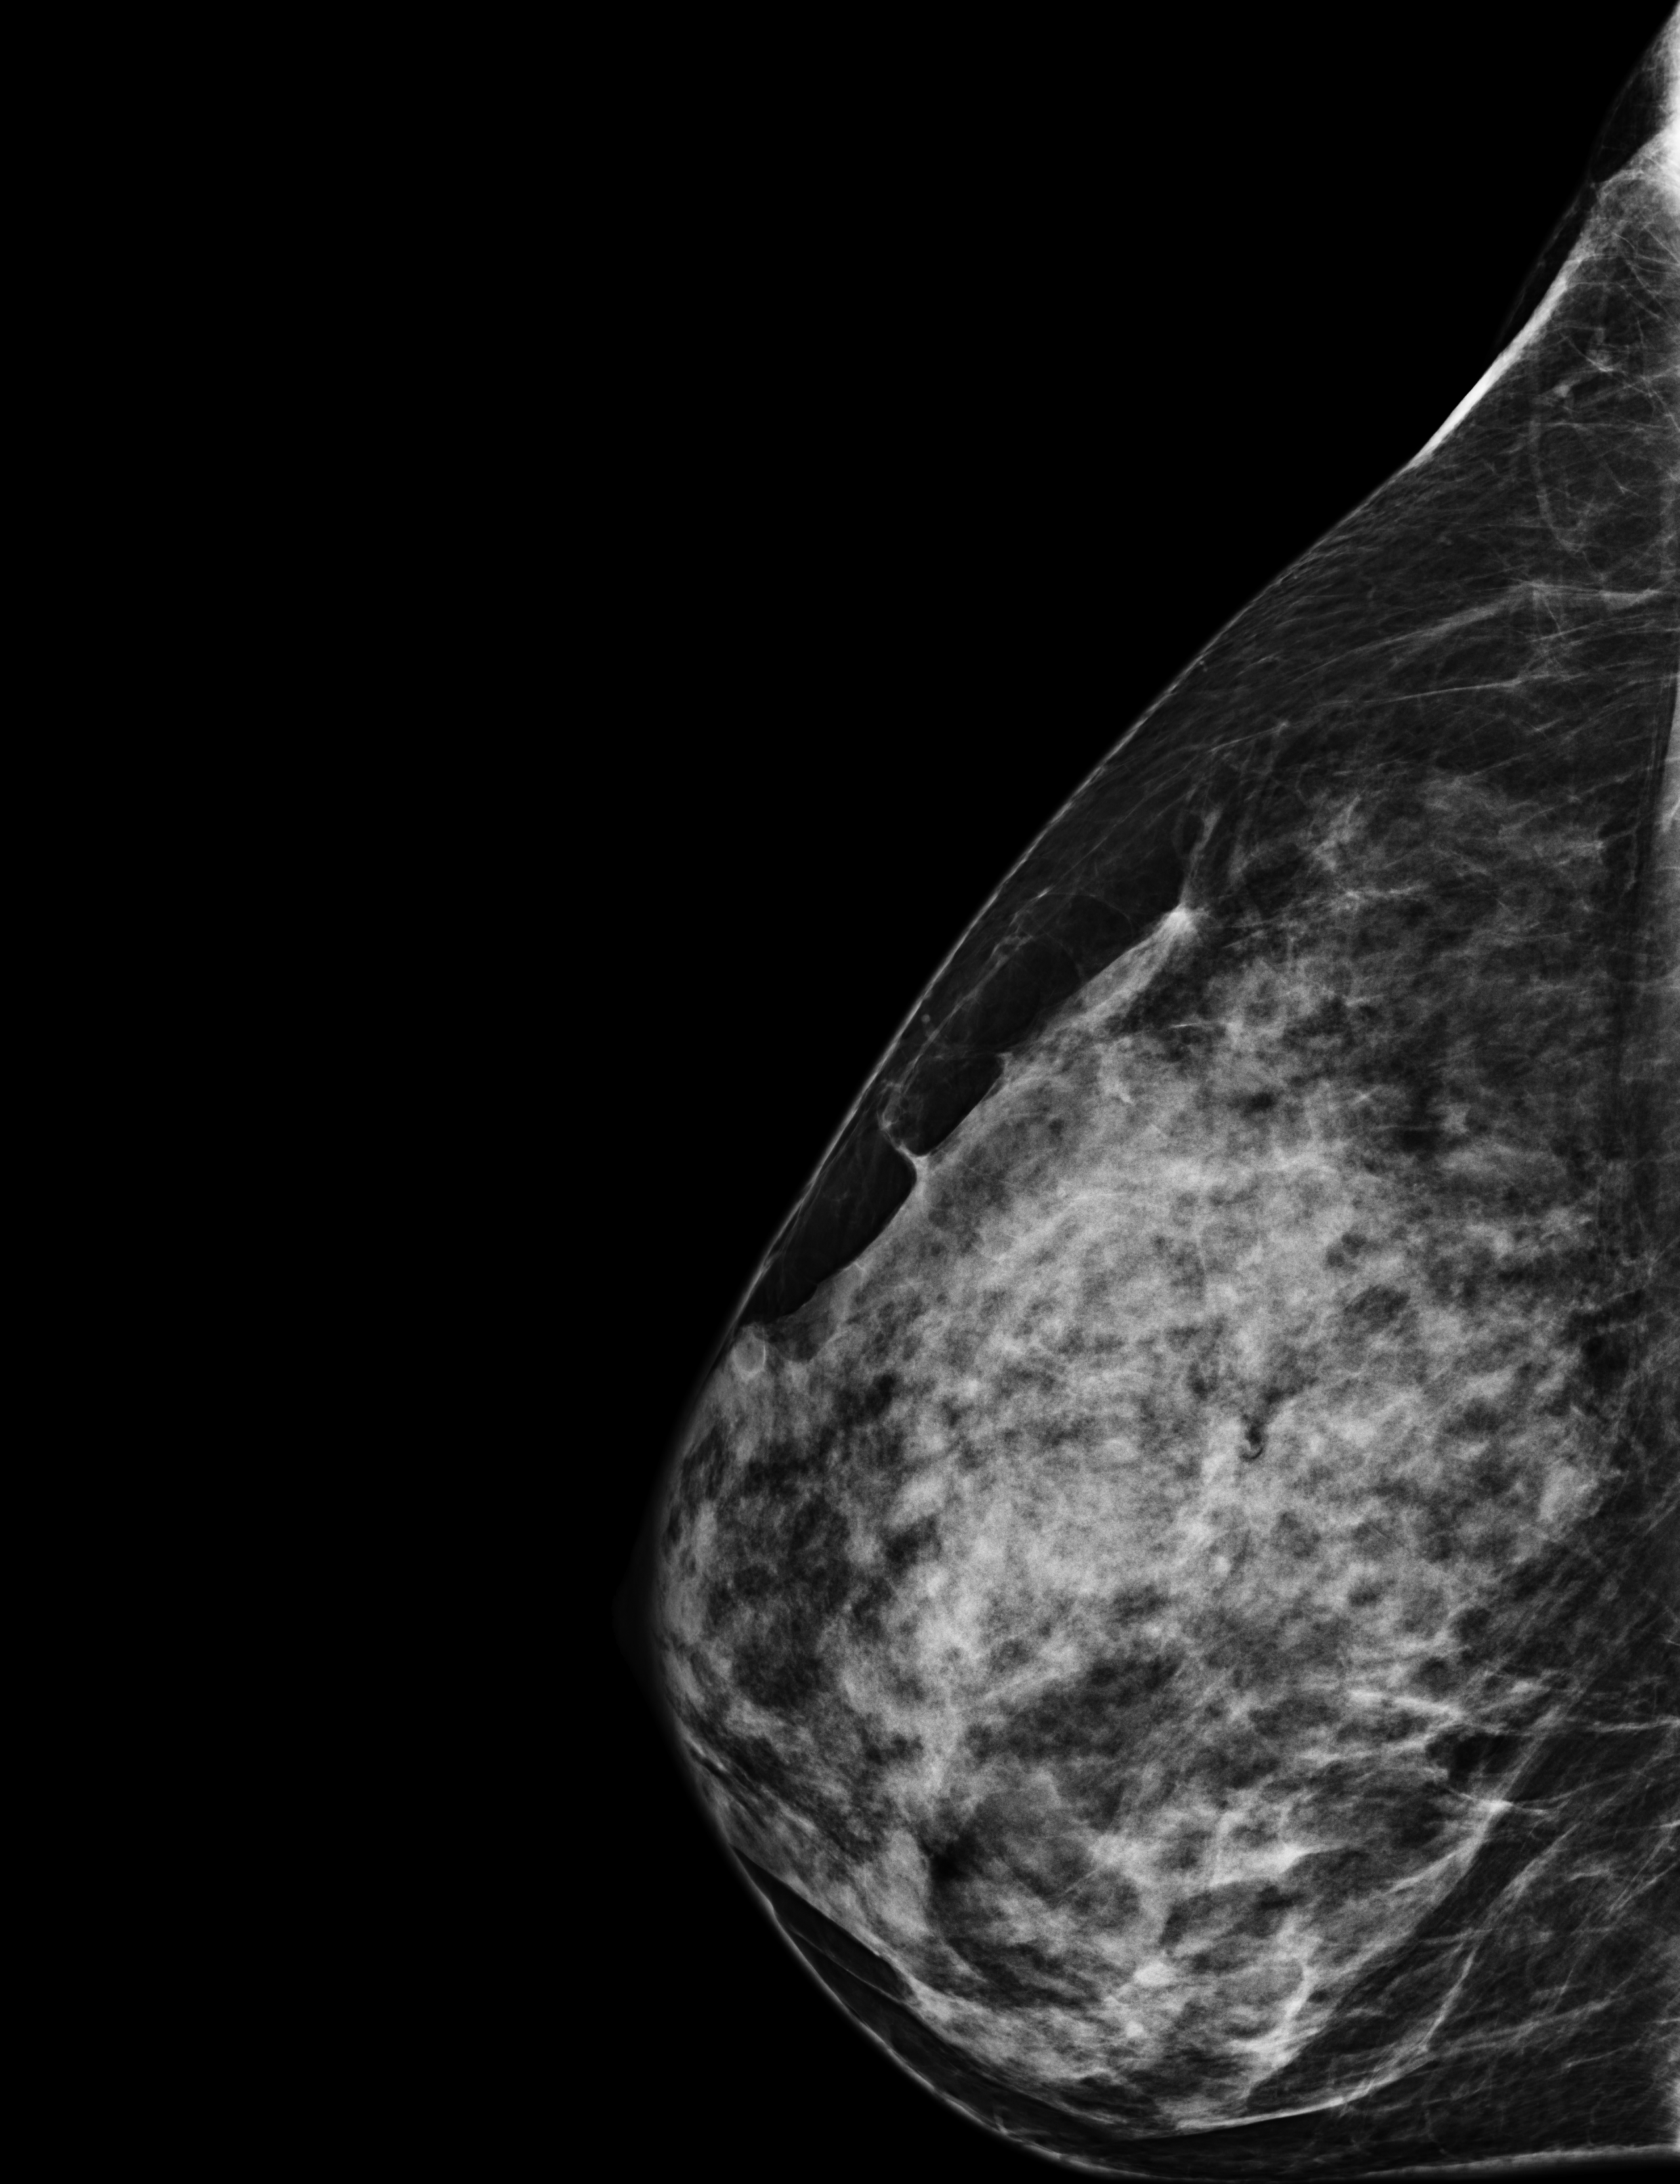
Digital mammogram (FFDM); right breast; exaggerated CC view (lateral); screening examination; system: Selenia Dimensions. Patient aged 42 years (female).
BI-RADS breast density category at the screening exam (both breasts, scale 1–4): 4. Final BI-RADS category for the screening round (tomosynthesis exam, both breasts): category 1. Recall: no recall after this screen.